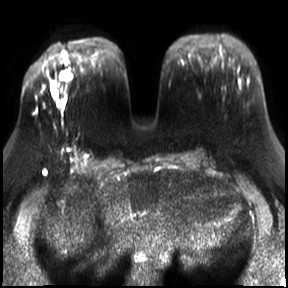
Breast MRI, one axial slice. Position 10 of 30 along the scan axis. Diffusion-weighted series; image 2 of 4 stored at this slice position (different b-values; order by instance number). 3 T. 4 mm slice thickness. 288 × 288 image matrix, field of view 340 × 340 mm. Female patient.
Structures marked on this image (manually delineated by an expert):
- tumour on diffusion-weighted imaging: box from (x=52, y=82) to (x=55, y=87) px